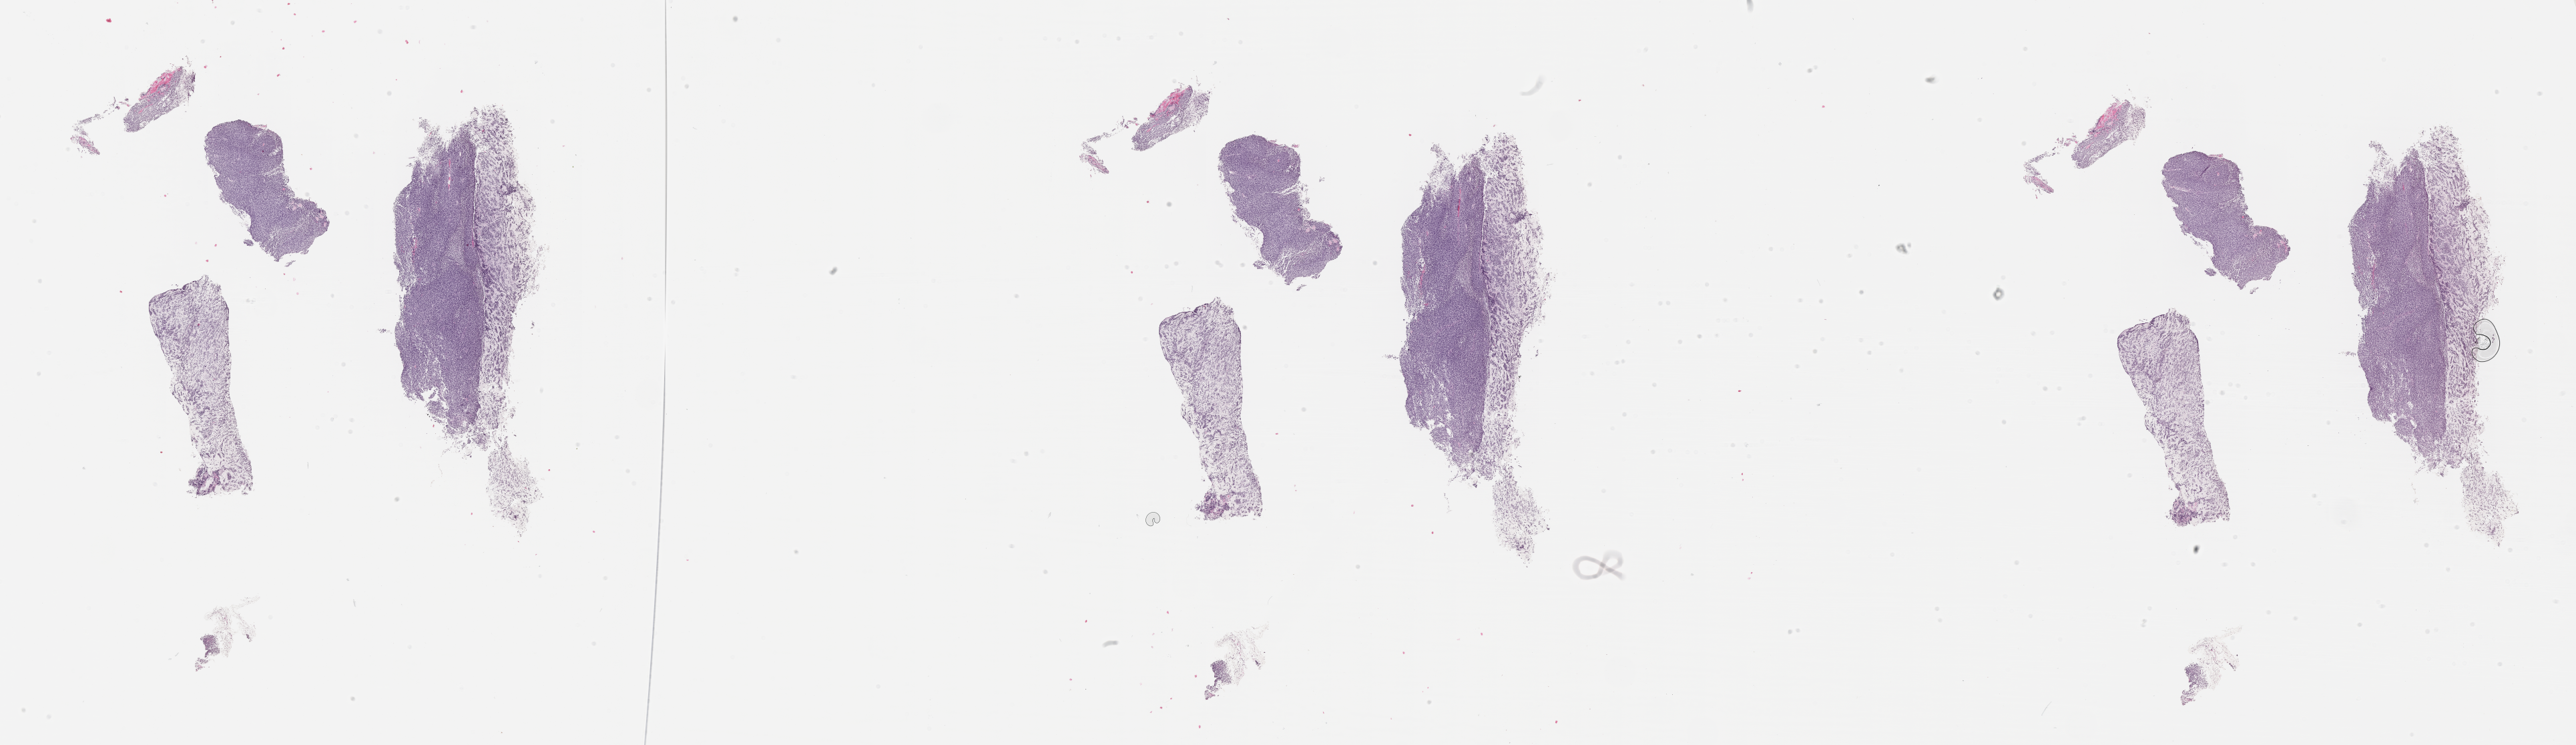
Whole-slide image, hematoxylin and eosin (H&E) stain of tumor tissue — whole scanned area (about 31.2 x 9.0 mm) shown as a low-resolution overview; formalin-fixed, paraffin-embedded (FFPE) tissue; sample anatomic site: bone, mandible-right (pterygoid muscle). Female patient, age at diagnosis 7.5 years.
Stage (as recorded): 3. Primary site (case record): infratemporal fossa (PM). Diagnosis: rhabdomyosarcoma; histological classification: embryonal rhabdomyosarcoma. Metastatic status at presentation (as recorded): non-metastatic (confirmed).